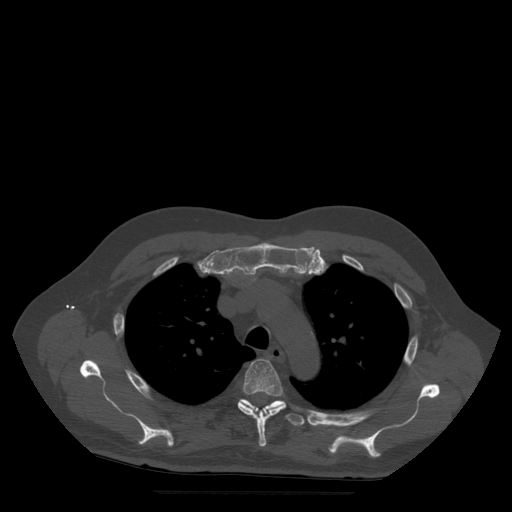
CT including the spine, one axial slice. Position 386 of 522 along the scan axis. Bone window (W 1800 / L 400 HU). 512 × 512 image matrix, field of view 420 × 420 mm. Patient age 72 years. Case-level facts recorded for this patient, not image findings: primary cancer: prostate.
Outlined on this slice (semi-automatic segmentation, software-assisted and operator-edited):
- T4 vertebra: box from (x=238, y=360) to (x=286, y=447) px
- T5 vertebra: (x=239, y=400)–(x=313, y=426)